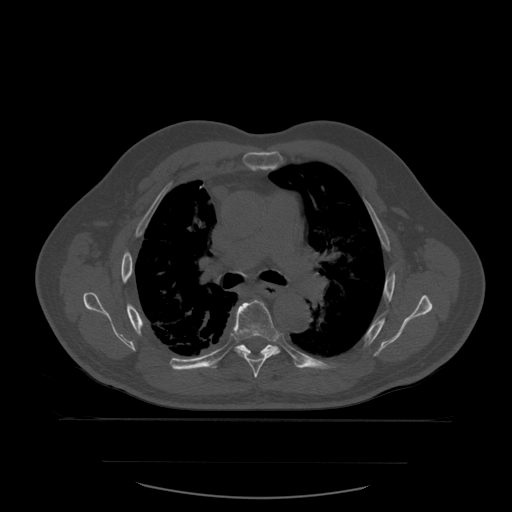
CT including the spine, one axial slice; position 398 of 590 along the scan axis; bone window (W 1800 / L 400 HU); 1.25 mm slice thickness; 512 × 512 image matrix, field of view 479 × 479 mm. Patient age 71 years. From the clinical record (not read from this slice): primary cancer: lung; vertebrae with lytic lesions (as recorded): T1, T2, L5, S1.
Structures marked on this image (semi-automatic segmentation, software-assisted and operator-edited):
- T6 vertebra: box from (x=234, y=300) to (x=280, y=378) px
- T7 vertebra: (x=235, y=344)–(x=281, y=354)